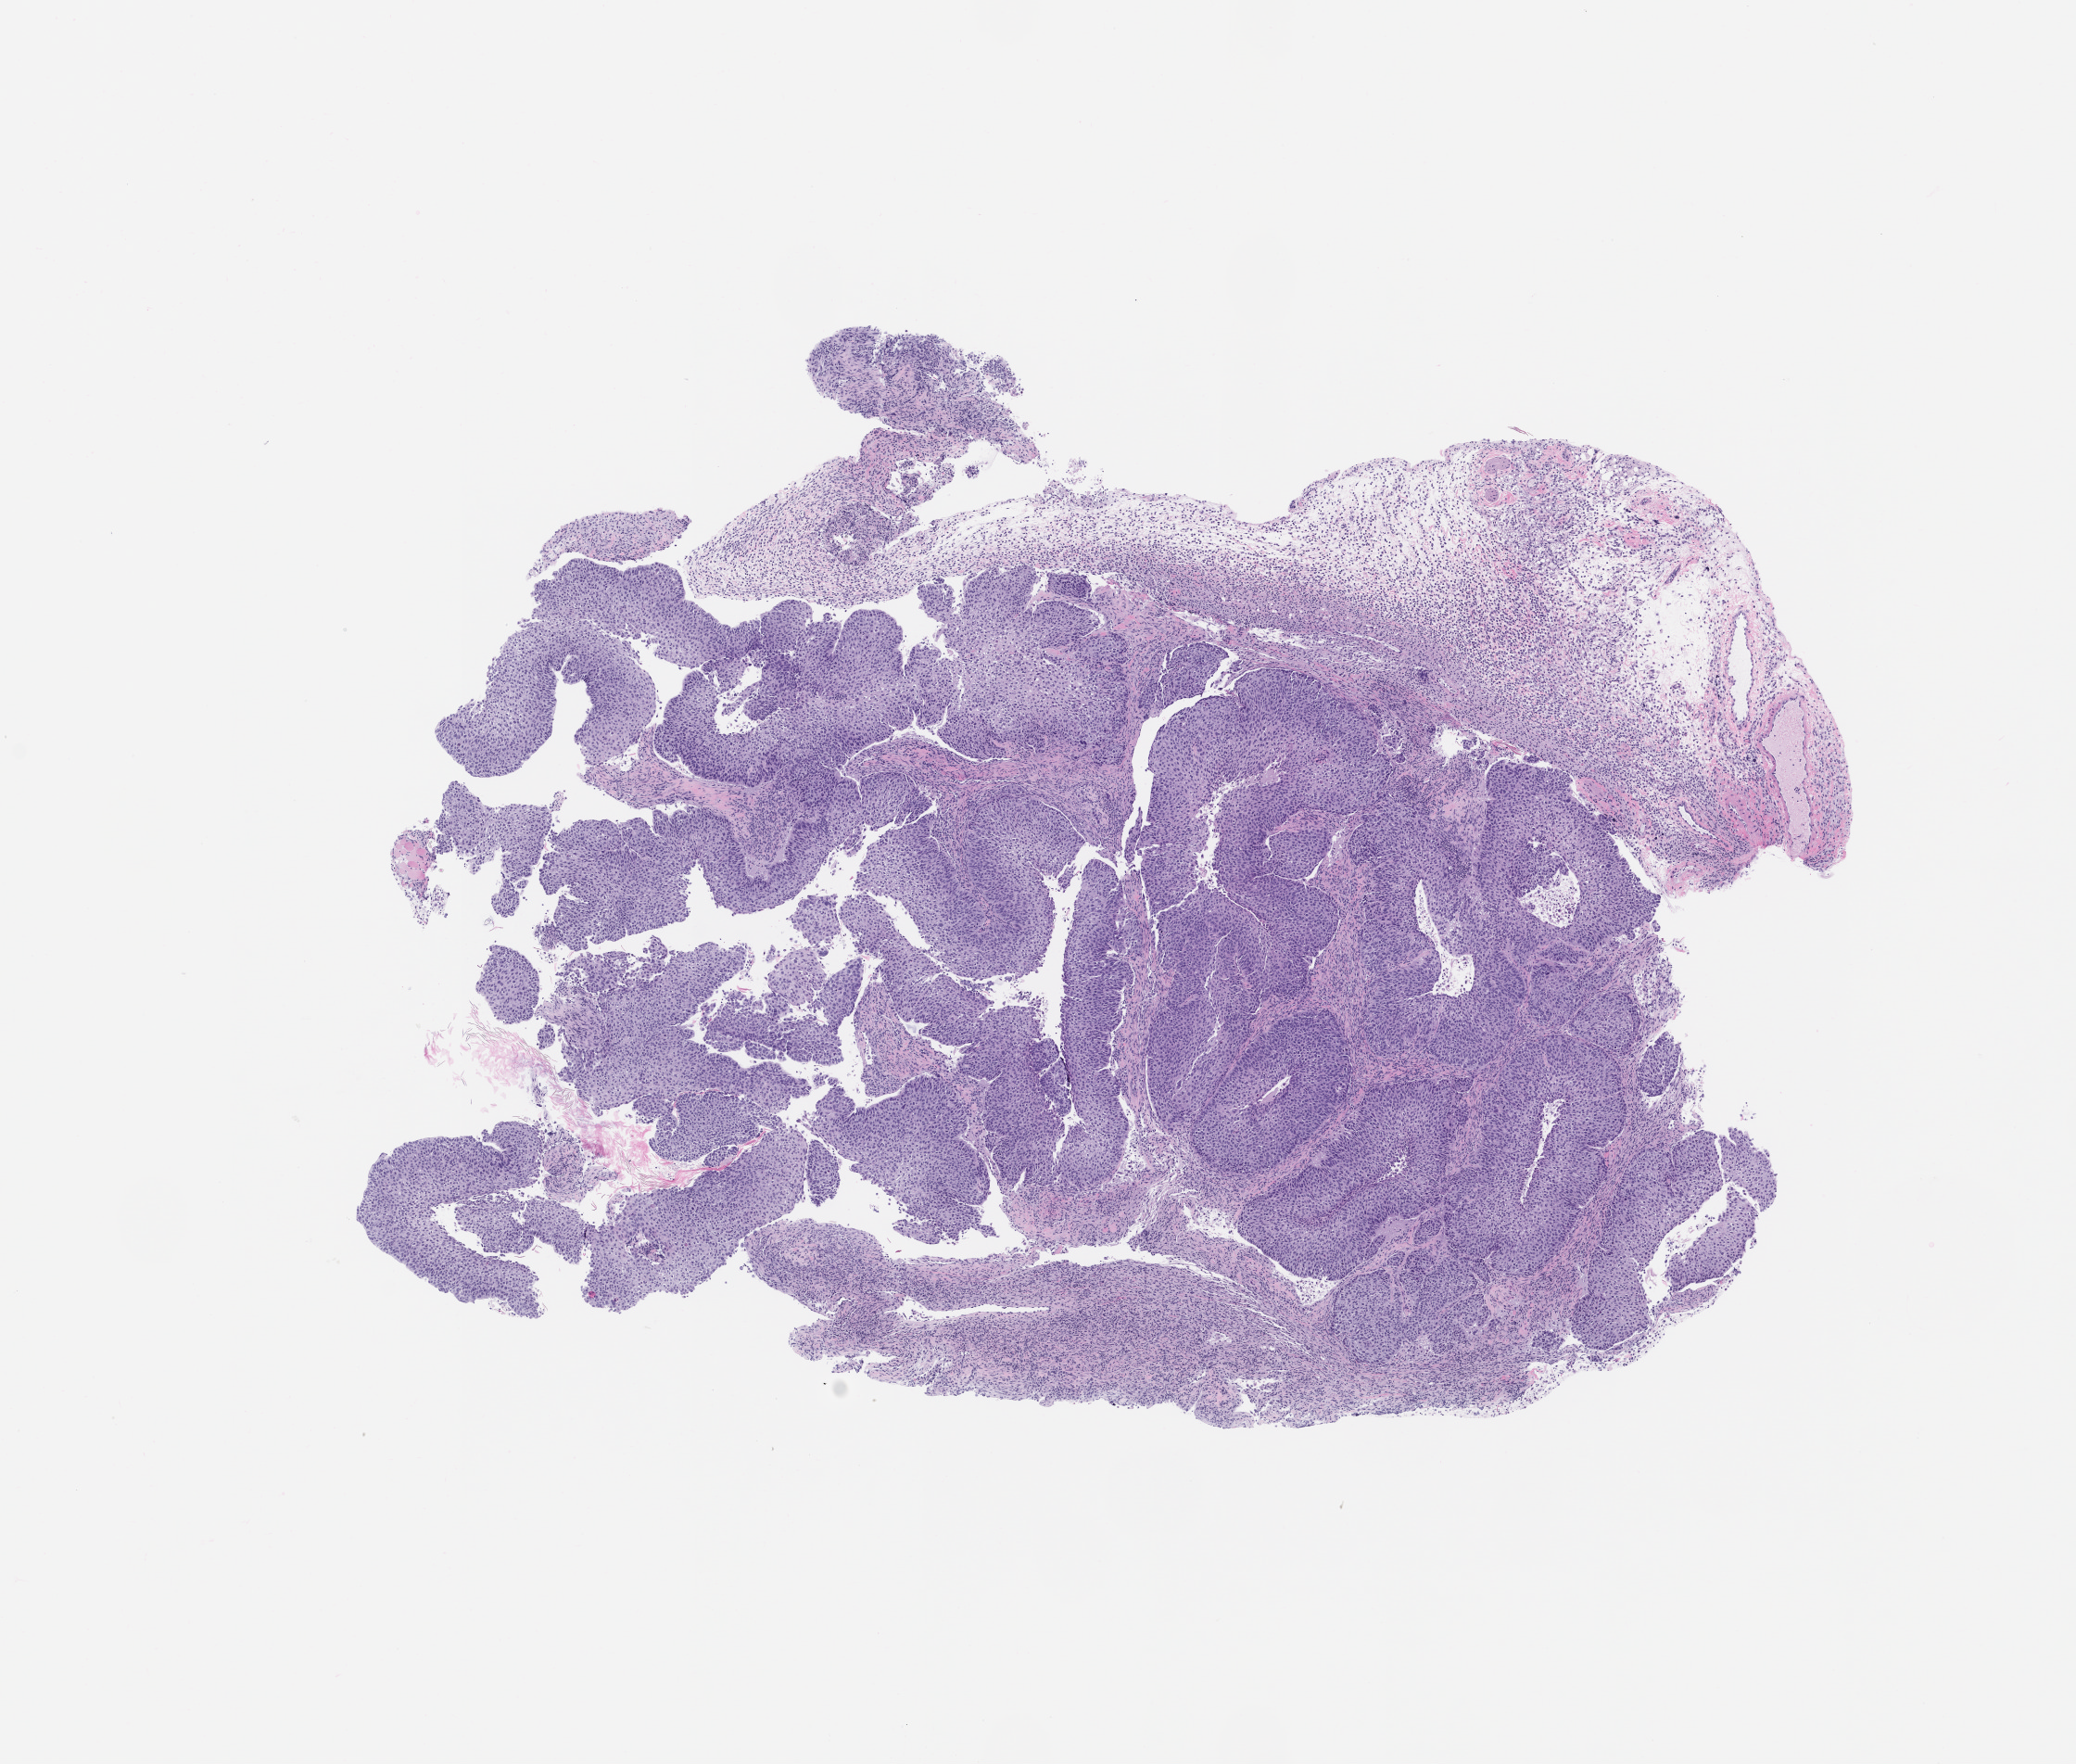
Whole-slide image, hematoxylin and eosin (H&E): patient-derived xenograft (human tumor grown in a mouse), passage 2 — shown as a low-resolution overview of the whole scanned area (about 9.0 x 7.6 mm). Formalin-fixed paraffin-embedded section. Tumor site category: lung.
- originating patient diagnosis: Lung Squamous Cell Carcinoma